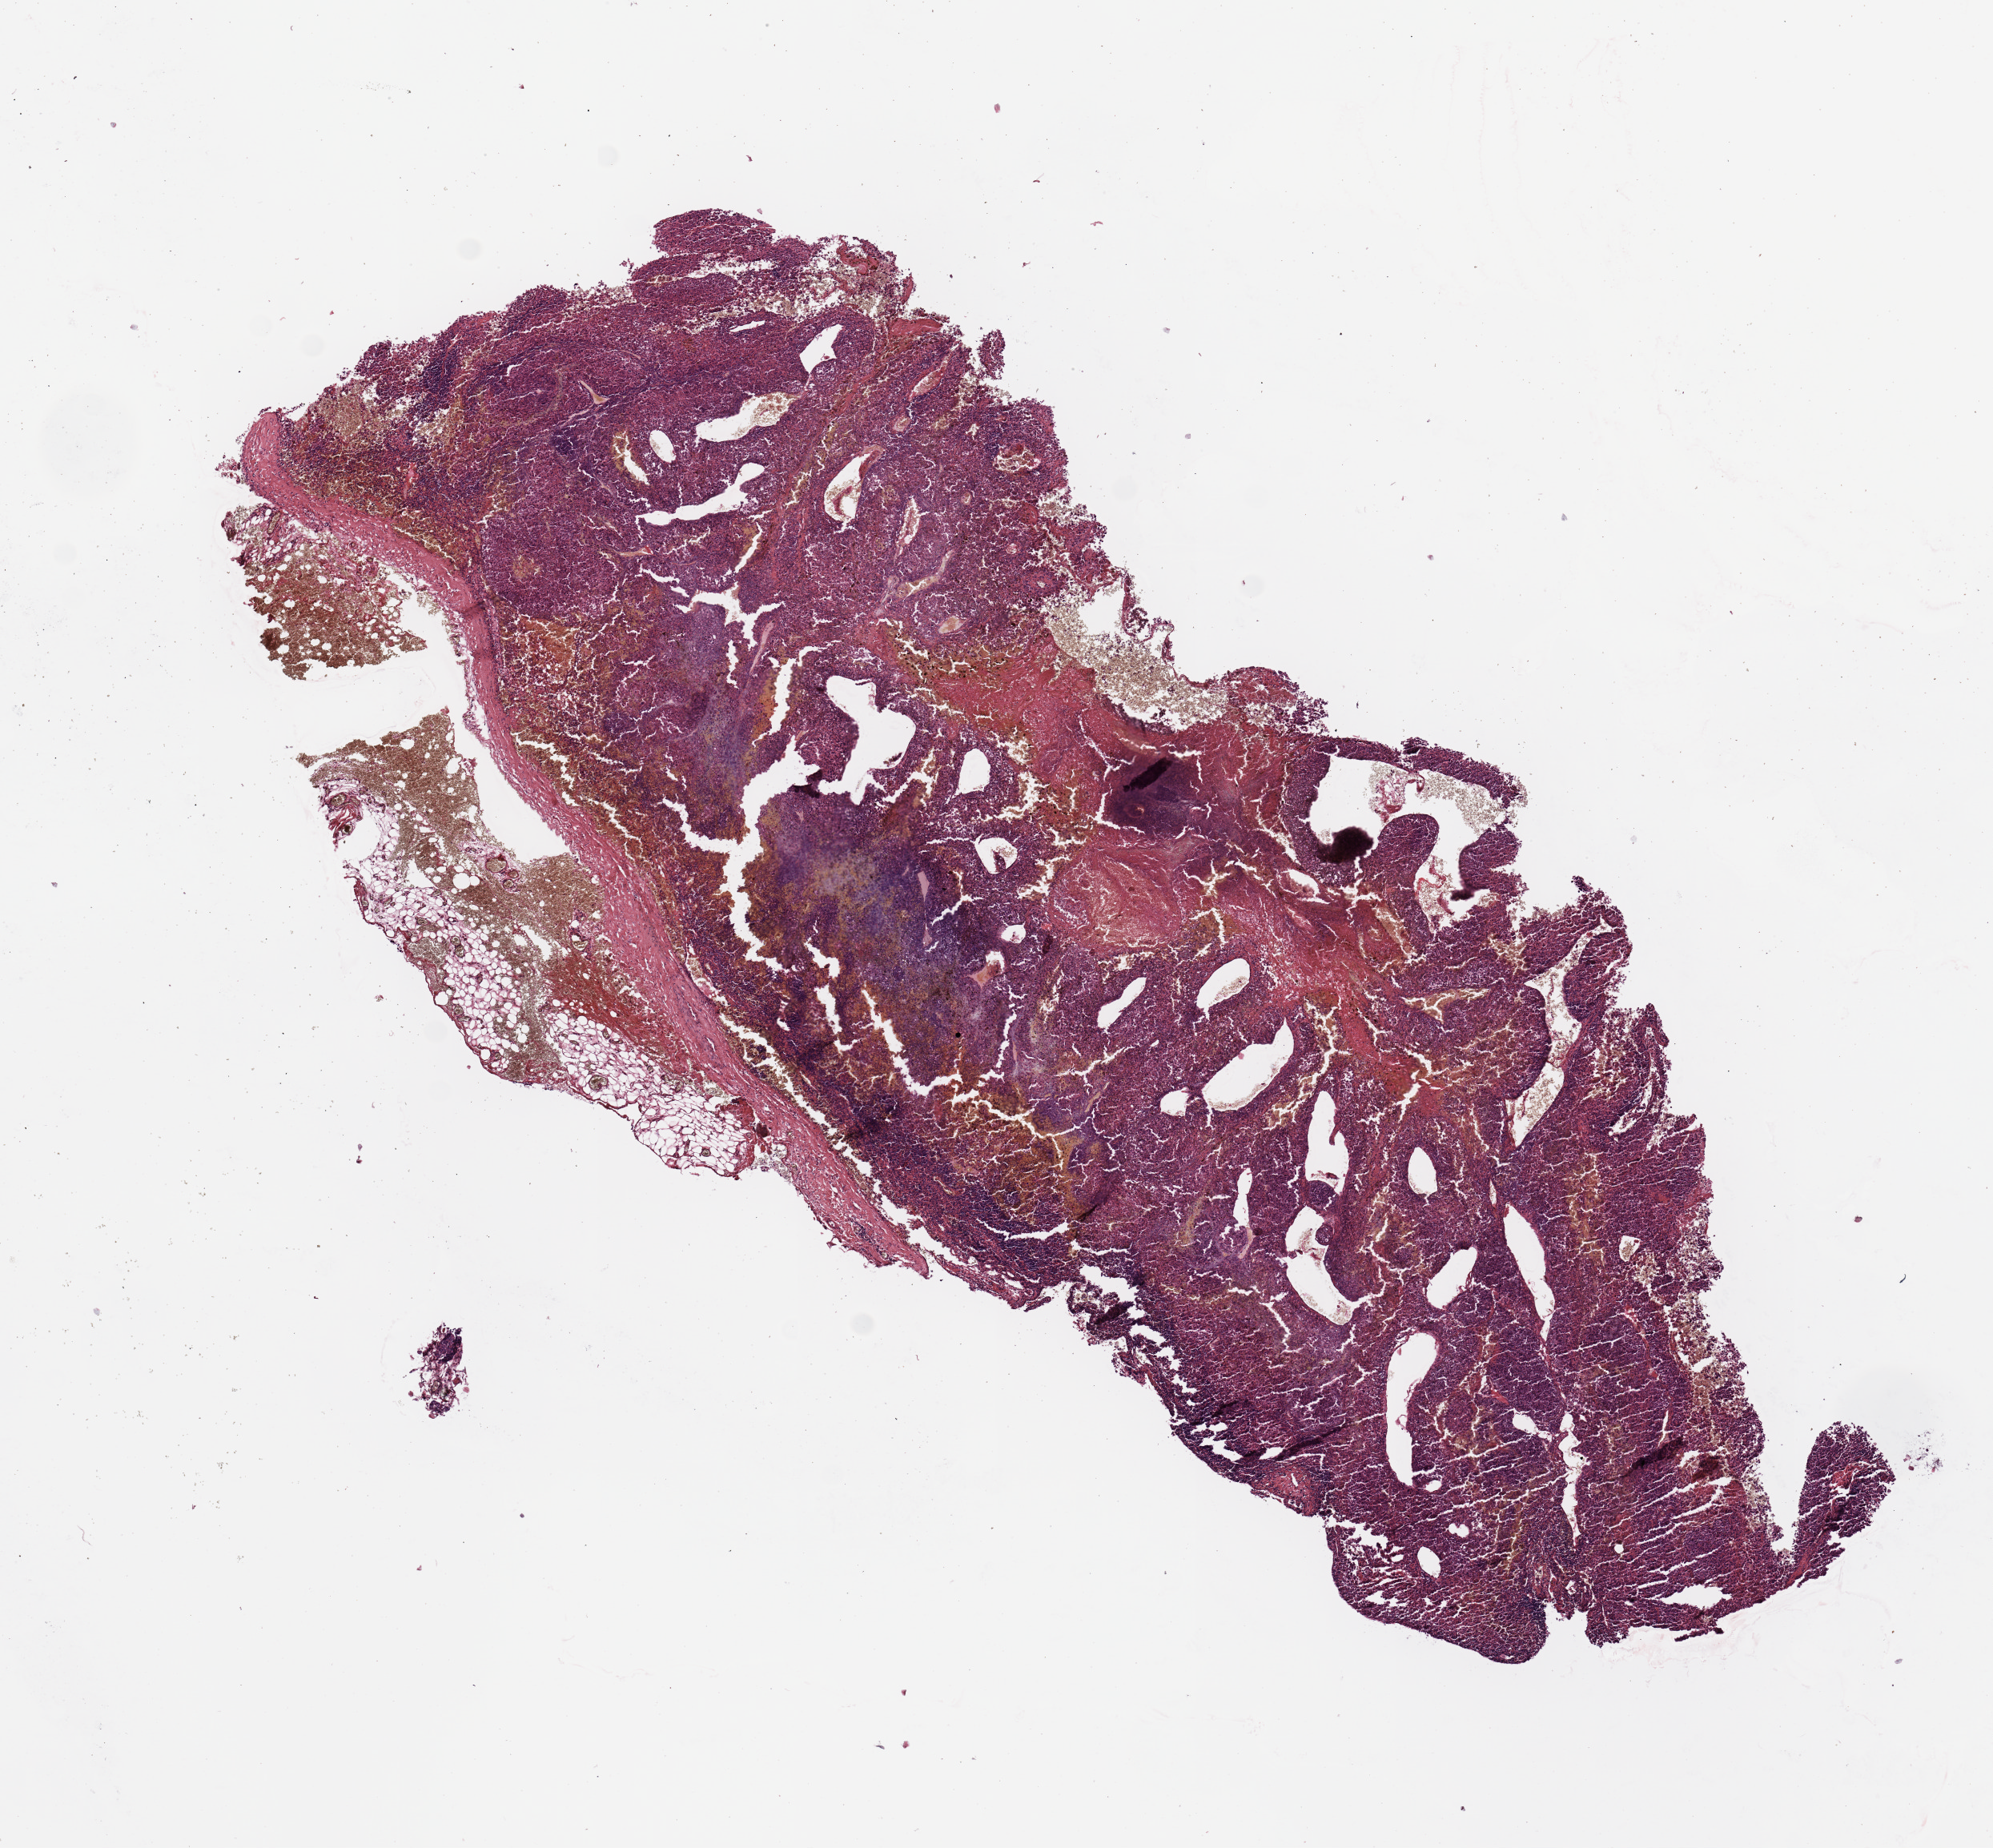
Digitized Hematoxylin and eosin (H&E) stained tissue section (whole slide) — low-resolution overview of the scanned area, about 9.8 x 9.1 mm (from a 20x scan); melanoma tumour tissue; sampled site not recorded. Male, 60 y/o.
• patient diagnosis (cohort enrolment): cutaneous melanoma (skin)
• primary tumour site (as recorded): extremities